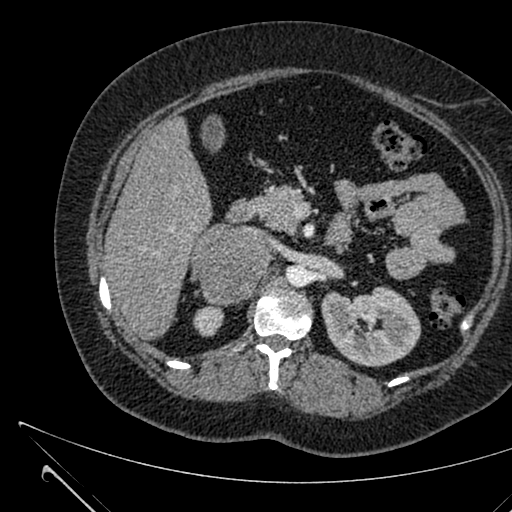
Contrast-enhanced abdominal CT, one axial slice; position 387 of 731 along the scan axis; 120 kVp; intravenous contrast given; soft-tissue window (W 400 / L 40 HU); 512 × 512 image matrix. Patient: female, 36 years. From the clinical record (not read from this slice): diagnosis: adrenocortical carcinoma; tumour side: right adrenal; tumour size at pathology: 10 cm; Ki-67 index: 20 %; stage (as recorded): 4.
Outlined on this slice (semi-automatic segmentation, software-assisted and operator-edited):
- mass: bounding box [x1, y1, x2, y2] px = [195, 226, 268, 303]